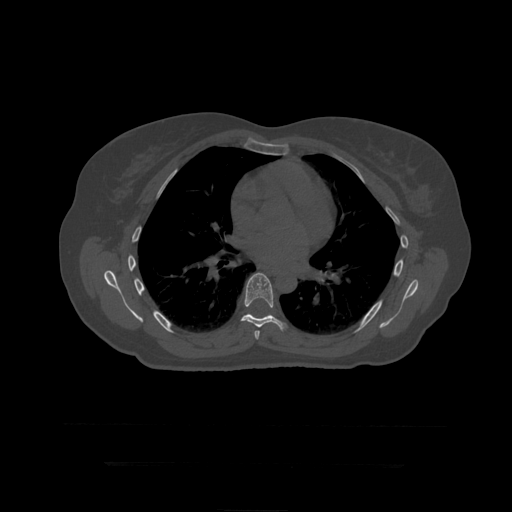
CT including the spine, one axial slice; slice 283 of 399 in the series (ordered by position); reconstruction kernel STANDARD; 120 kVp; bone window (W 1800 / L 400 HU); 1.25 mm slice thickness; 512 × 512 image matrix. Patient age 41 years. Case-level facts recorded for this patient, not image findings: primary cancer: breast.
Structures marked on this image (semi-automatic segmentation, software-assisted and operator-edited):
- T7 vertebra: bounding box <254,331,260,340> (left, top, right, bottom; pixels)
- T8 vertebra: <241,273,287,332>